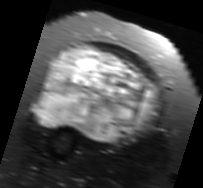
MRI of an extremity soft-tissue mass, one axial slice; position 43 of 91 along the scan axis; T2-weighted fat-saturated; MR volume resampled by the dataset authors to the PET/CT grid (not the native acquisition matrix); 3.27 mm slice thickness; 203 × 188 image matrix. Female patient. From the clinical record (not read from this slice): histological type: malignant solitary fibrous tumor; grade: intermediate; site of the primary tumour: right thigh.
Structures marked on this image (expert contour drawn on MRI and transferred to this co-registered scan by the dataset authors):
- gross tumour volume including surrounding oedema: box from (x=31, y=44) to (x=162, y=143) px
- gross tumour volume (mass): (x=37, y=44)–(x=157, y=141)